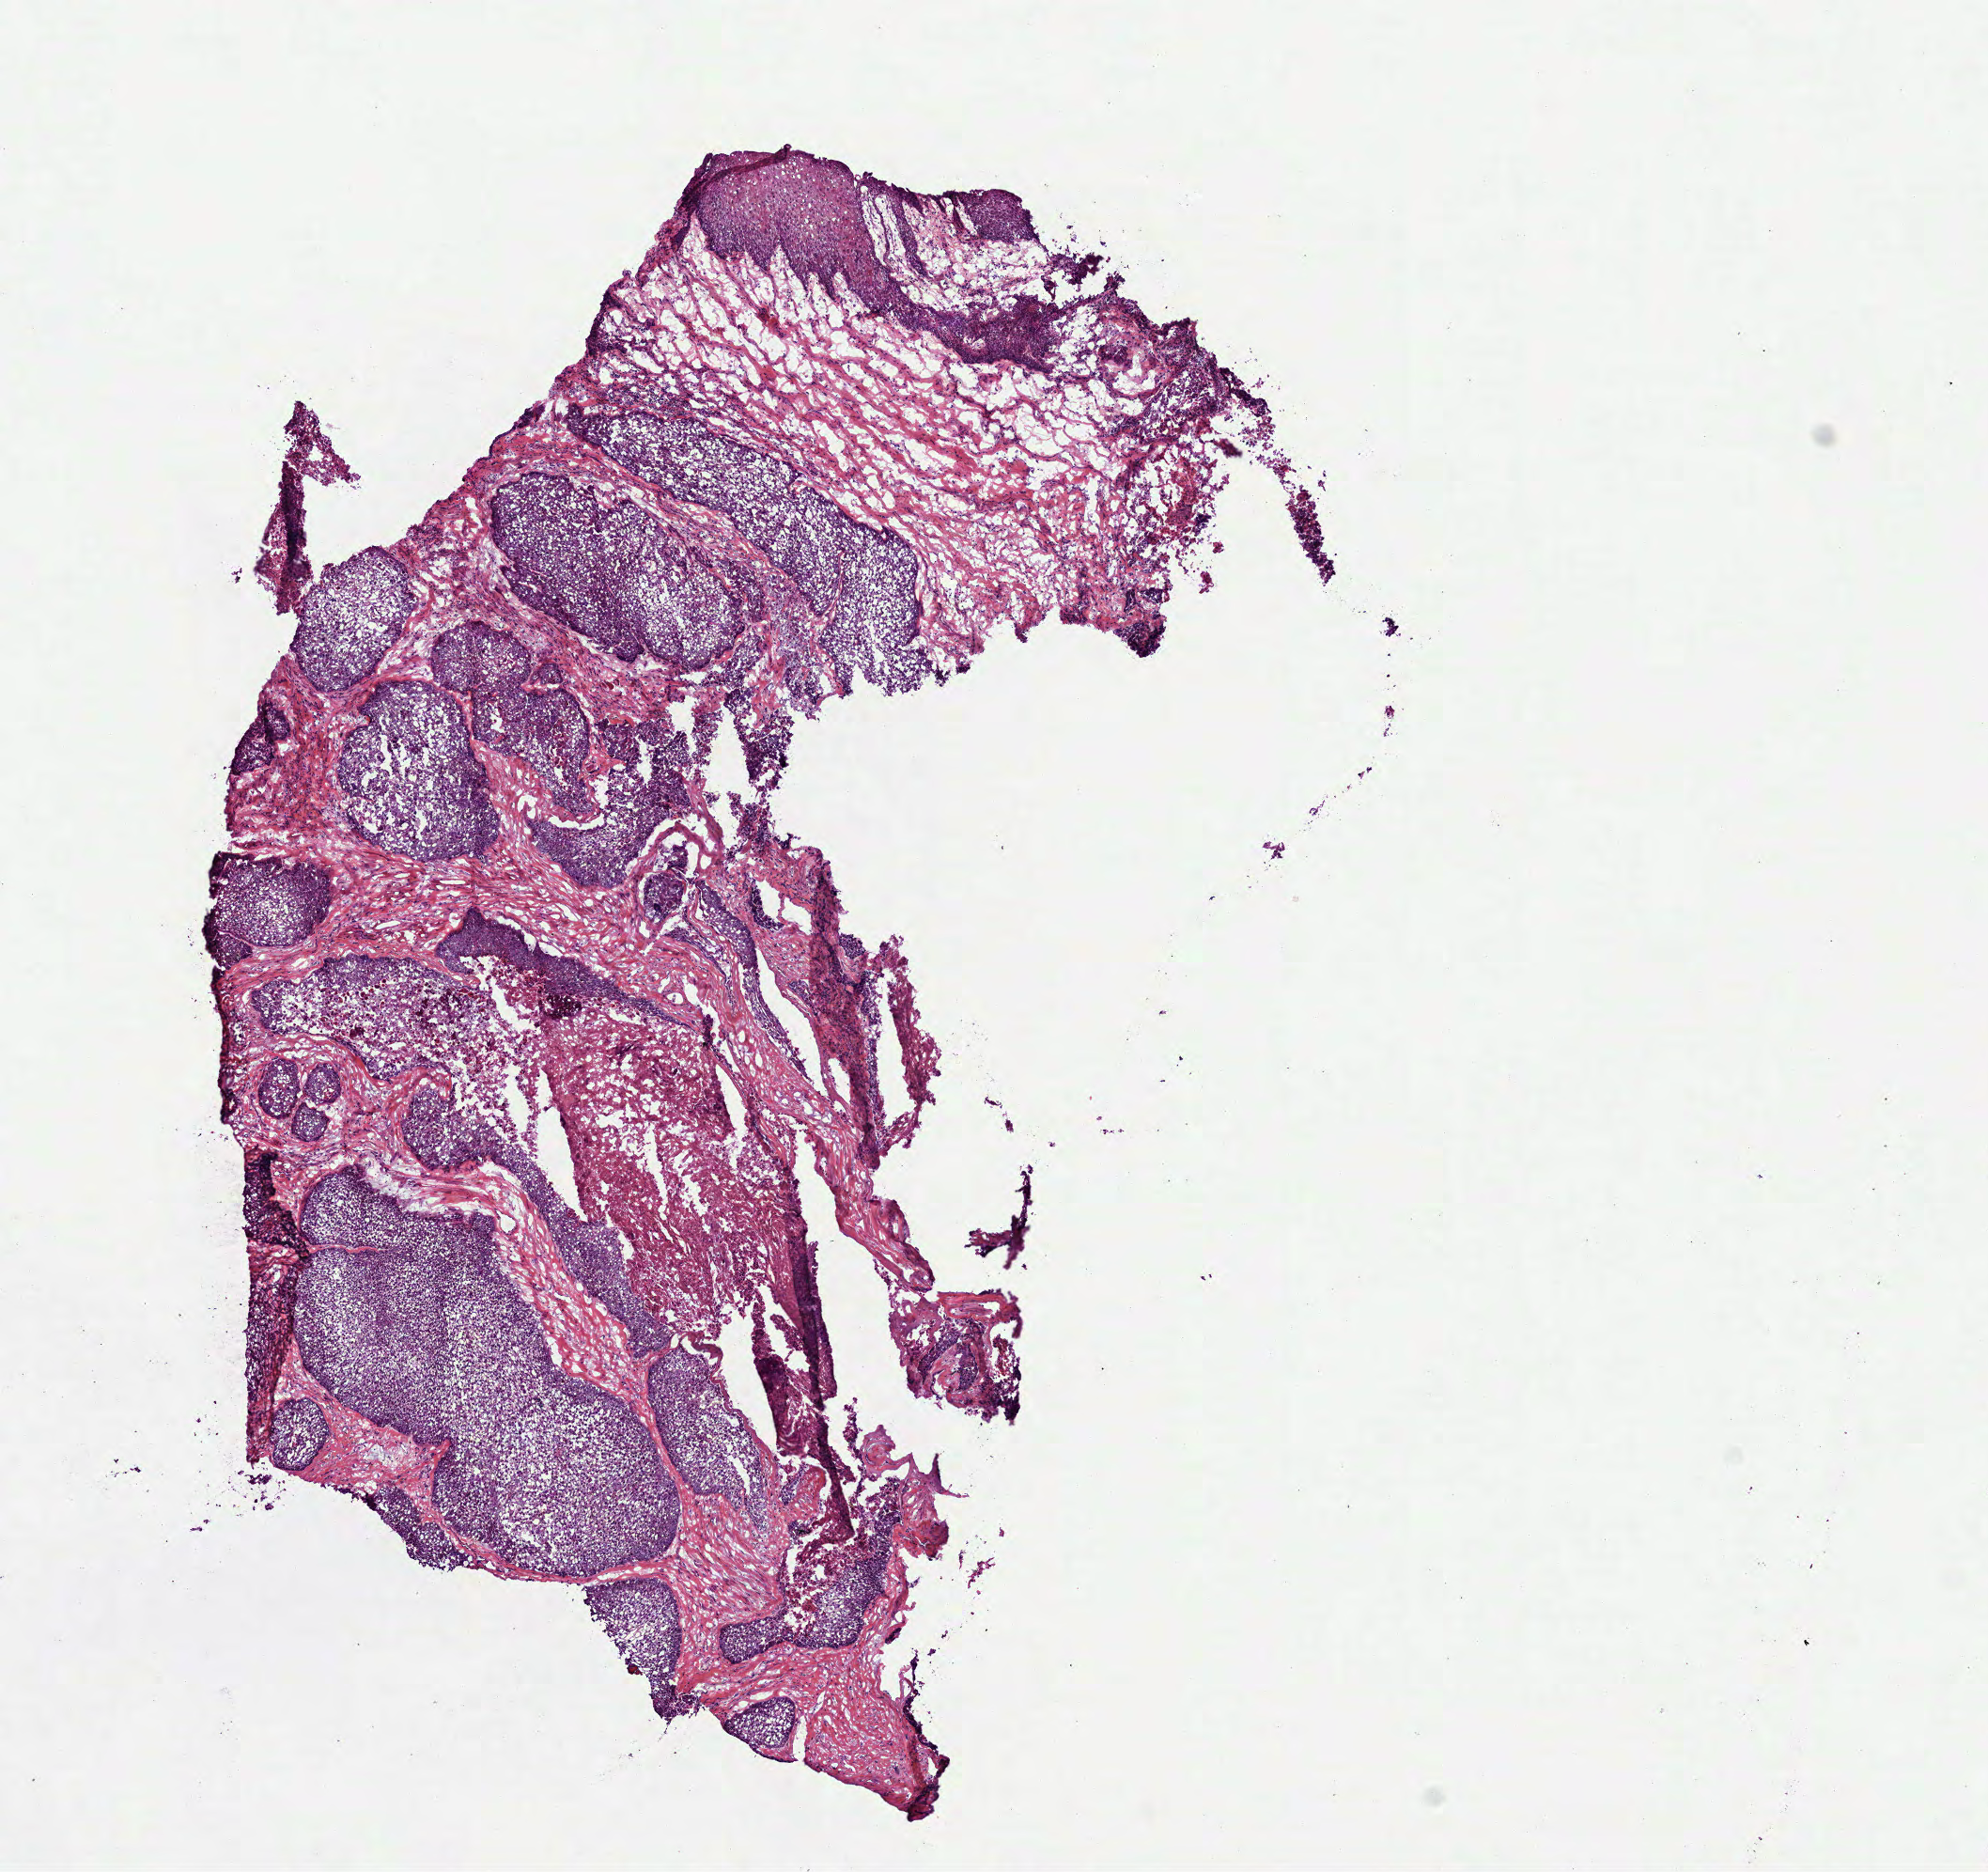
Whole-slide histology image, H&E-stained, low-resolution overview of the scanned area, about 8.5 x 8.0 mm (from a 40x scan); frozen section; head and neck, primary tumour sample. Patient: male, age at initial diagnosis 65 years. Histologic grade: G2 (moderately differentiated). Composition of this section per pathologist review: tumour cells 58%, tumour nuclei 85%, normal cells 5%, stromal cells 35%, necrosis 2%.
Lymph nodes positive (case pathology): 0 of 25 examined. Diagnosis: Squamous cell carcinoma, NOS (overlapping lesion of lip, oral cavity and pharynx). AJCC pathologic stage: III (6th edition).